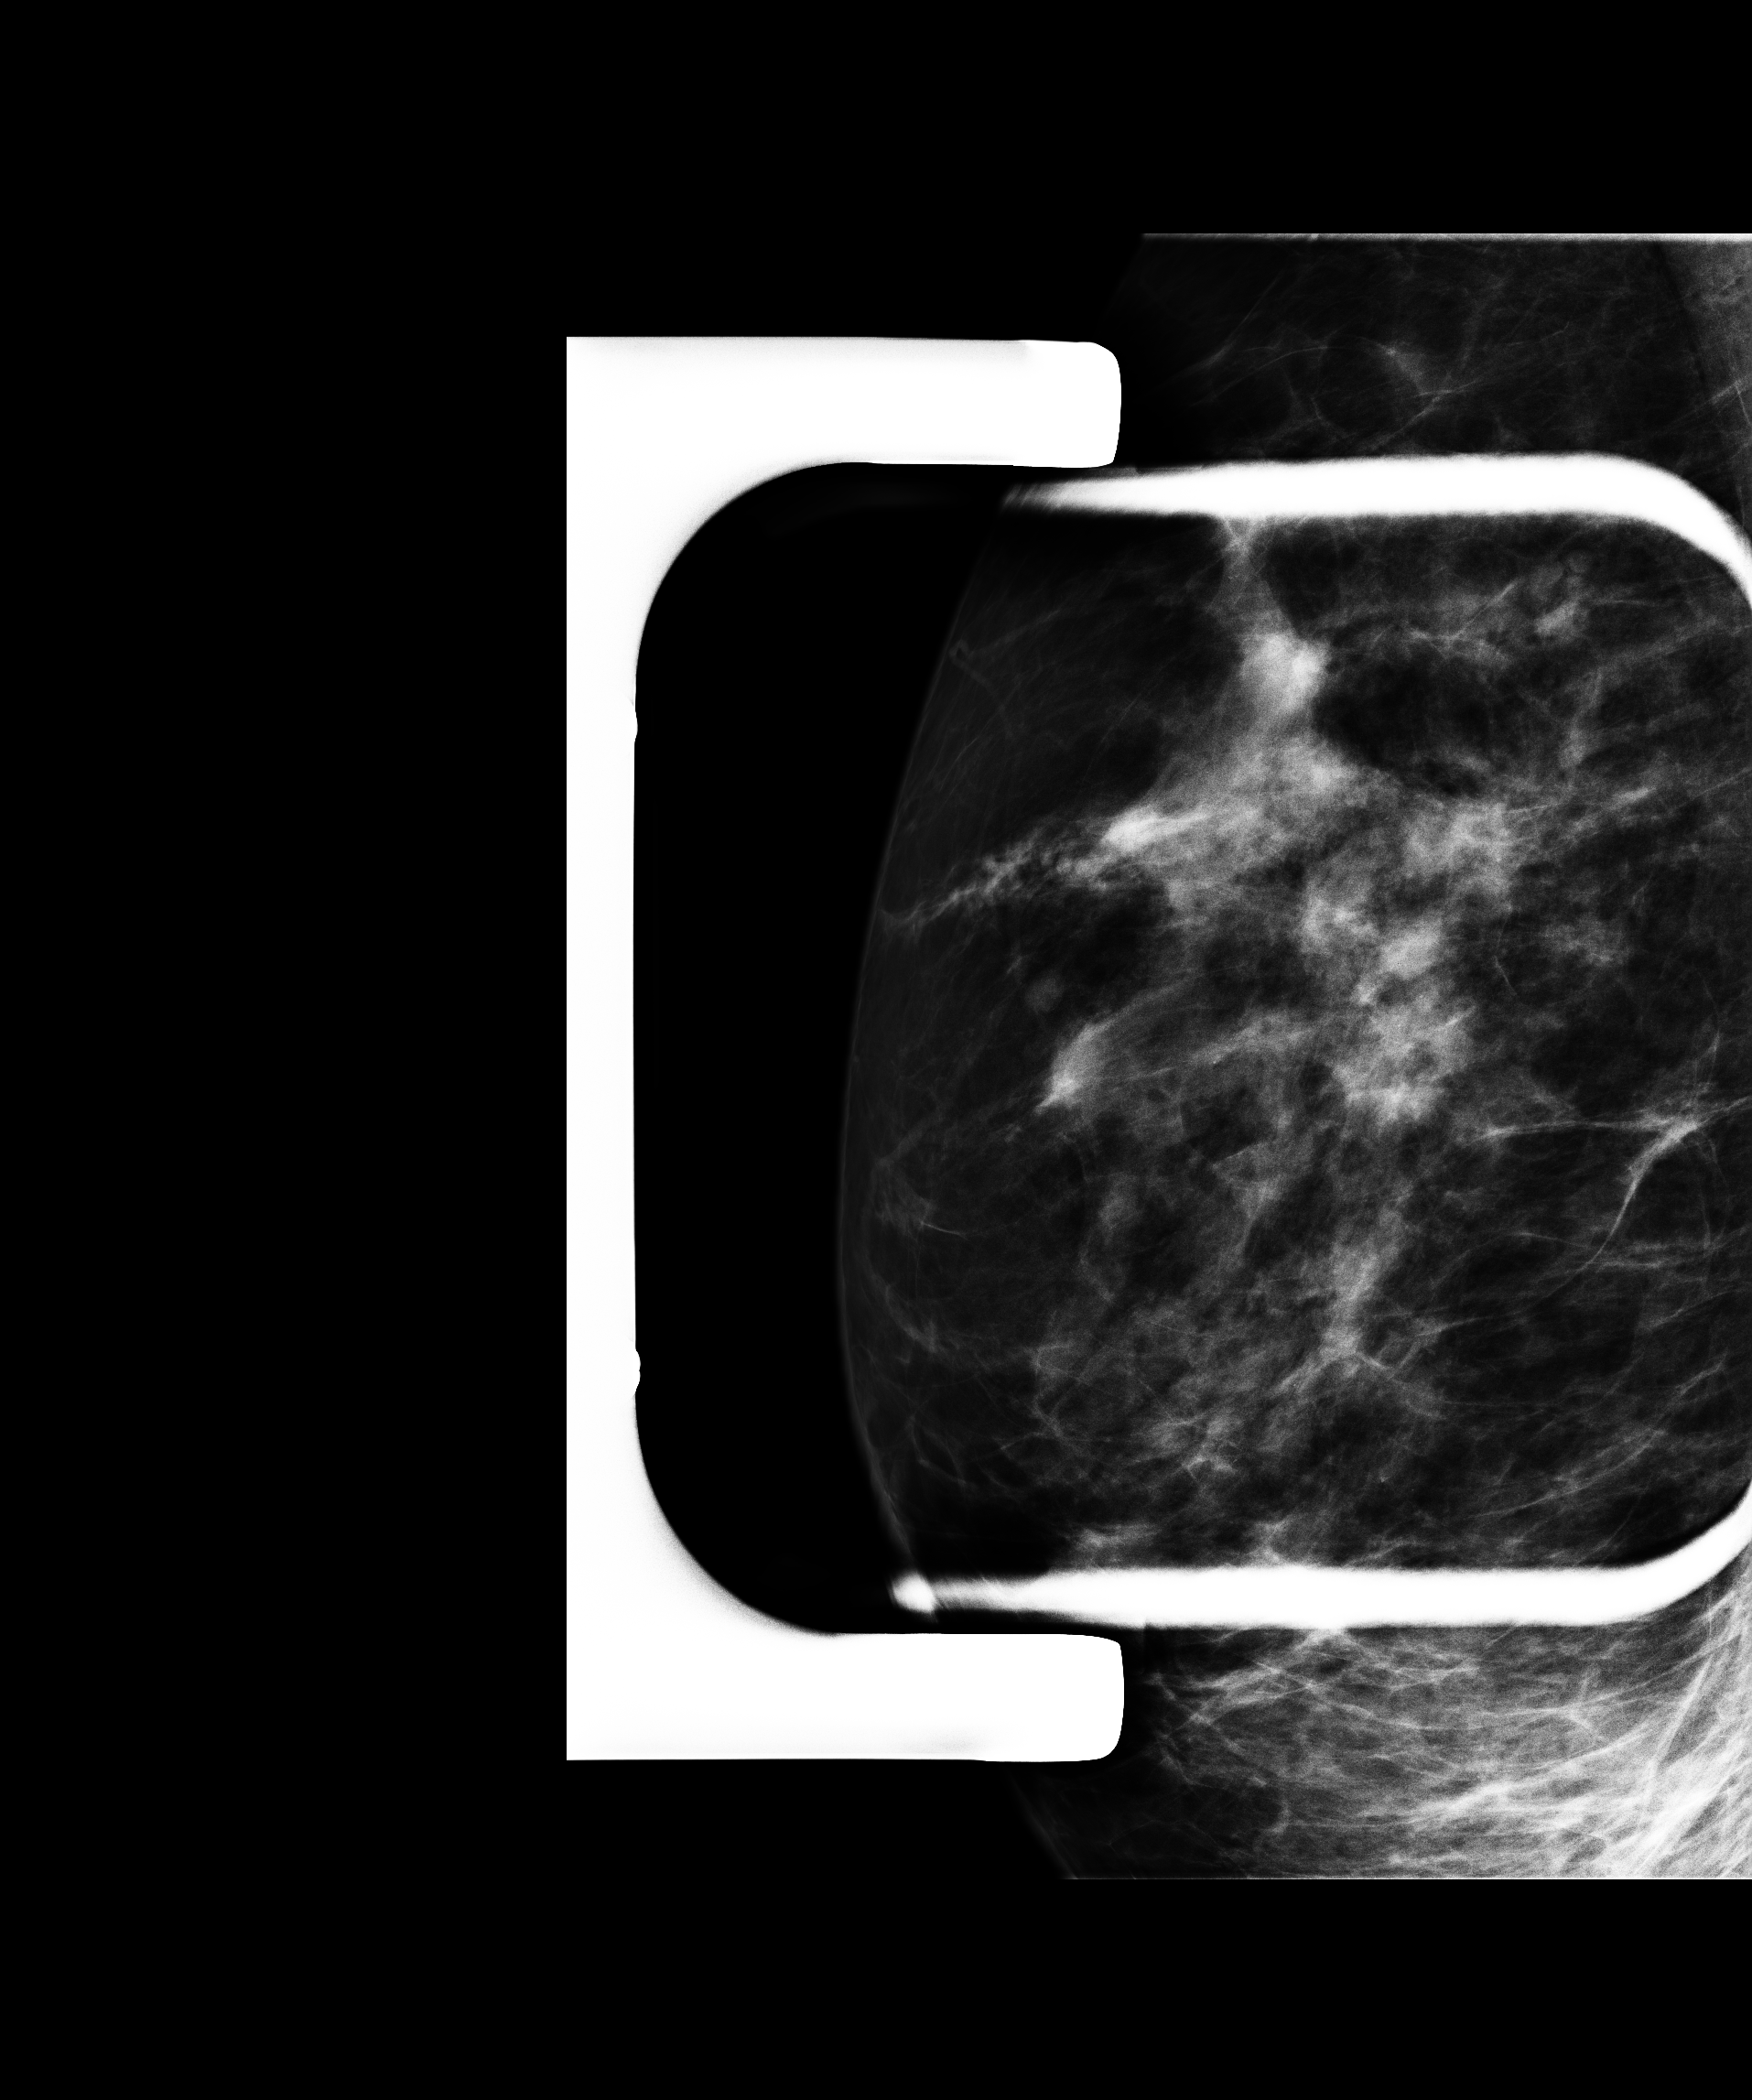
Additional (diagnostic) view; compressed breast thickness 55 mm.
Image type: full-field digital mammogram. Breast: right. Projection: mediolateral (ML) view, spot compression.